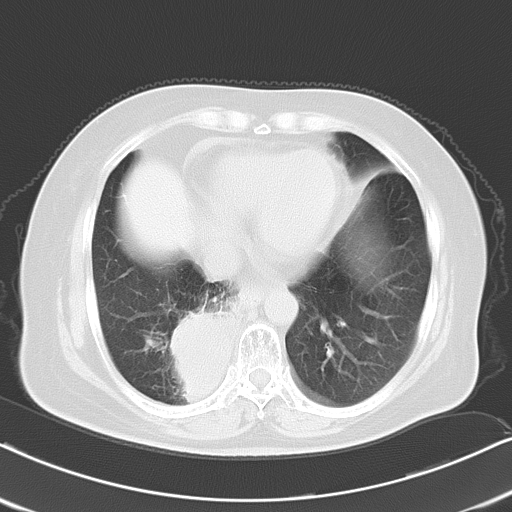
Chest CT, one axial slice; position 6 of 21 along the scan axis; 120 kVp; lung window (W 1500 / L -600 HU); 512 × 512 image matrix. Patient: female, 61 years. From the clinical record (not read from this slice): clinical TNM (as recorded): T1b N0 M1b.
Structures marked on this image (rectangle marked by the reading radiologist):
- lung tumour (recorded histology: squamous cell carcinoma): box from (x=161, y=300) to (x=232, y=408) px